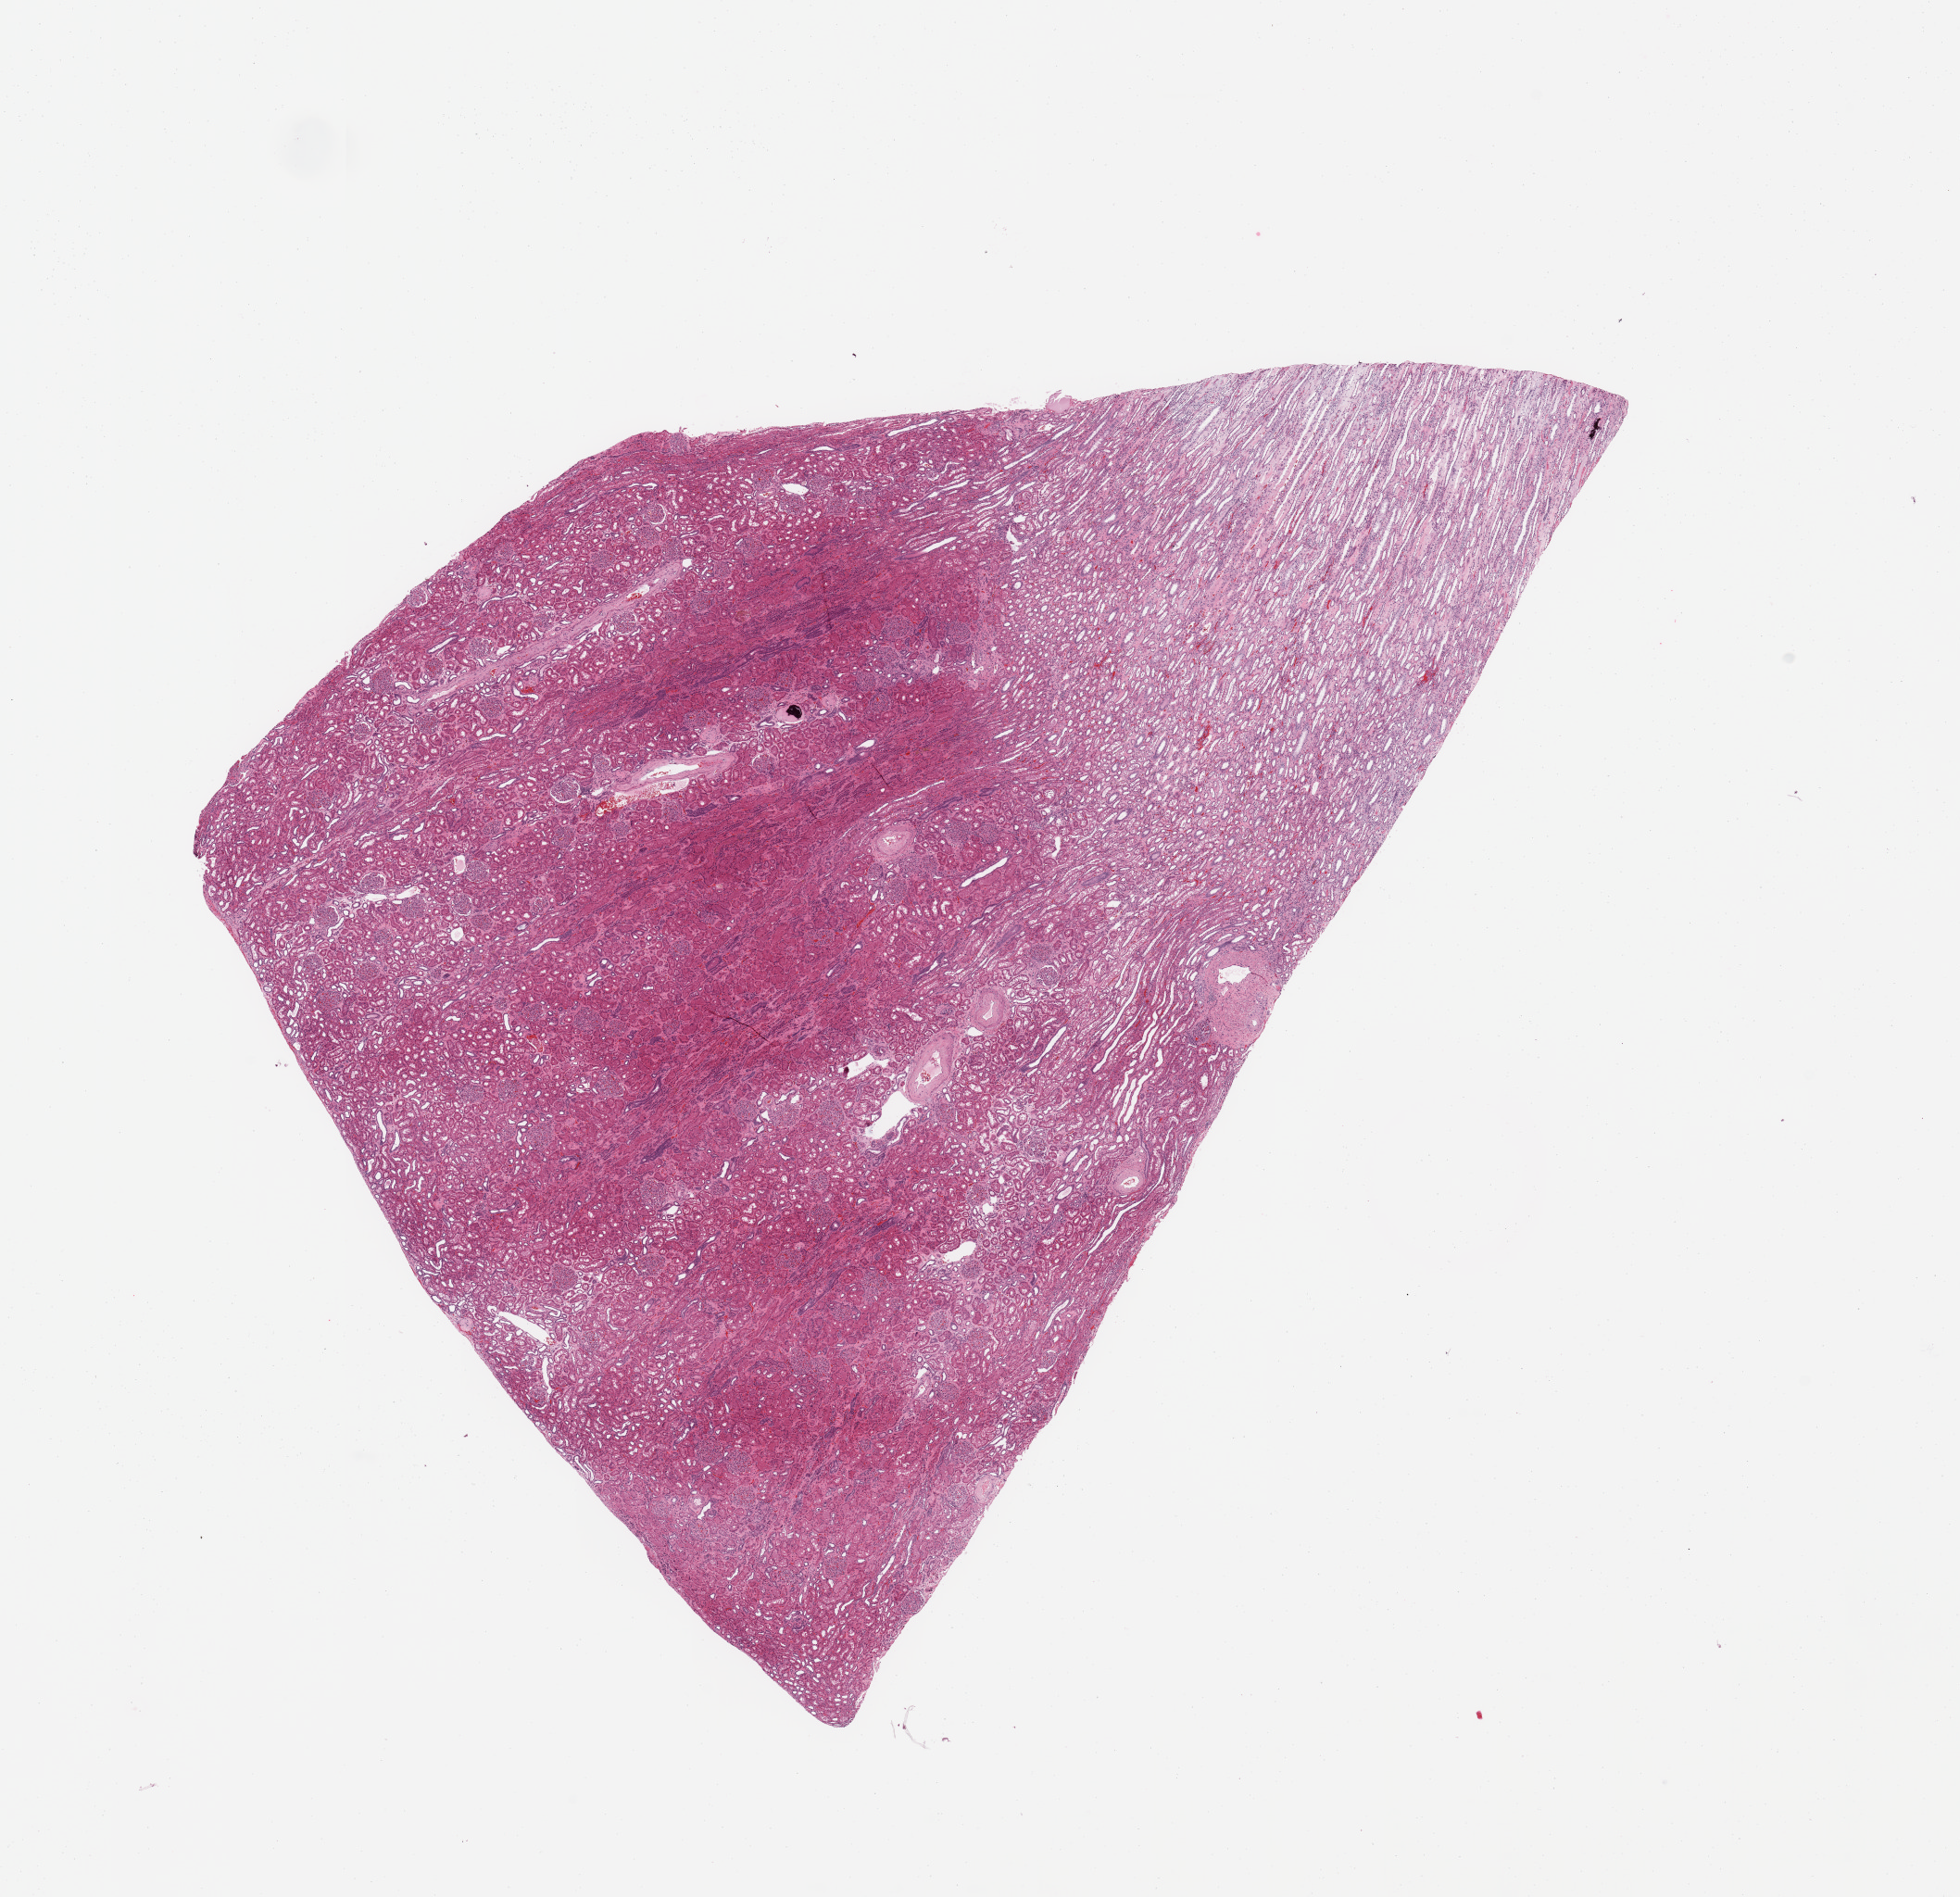
H&E whole-slide image — shown as a low-resolution overview of the whole scanned area (about 16.7 x 16.2 mm), normal (non-tumour) tissue sample, sampled site: kidney. 67-year-old female patient.
• this section: normal (non-tumour) tissue from the same patient
• patient diagnosis: Renal cell carcinoma, NOS